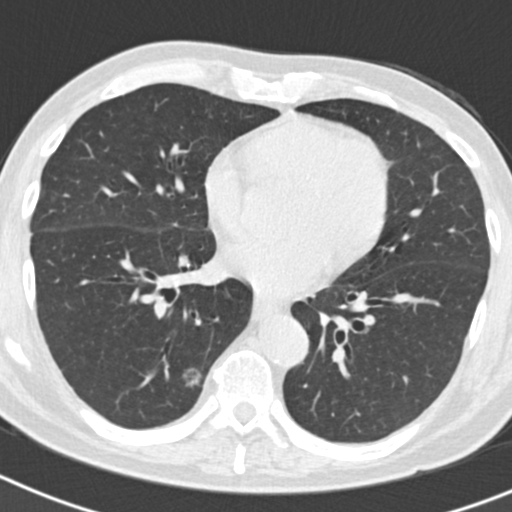
Low-dose screening chest CT, axial slice, second annual screen, lung window (W 1500 / L -600 HU), 2 mm slice thickness, standard (soft-tissue) reconstruction kernel (B30f). Male participant, aged 70 years at enrolment. Current smoker at enrolment.
Lesion marked by an expert reader, bounding box <124,356,209,429> (left, top, right, bottom; pixels). The screening reader recorded 5 non-calcified nodules or masses ≥4 mm on this exam (right lower lobe, right lower lobe, right upper lobe, right upper lobe, left upper lobe); which of them this box marks is not recorded. Official screen result: positive, other. Later outcome: lung cancer diagnosed 622 days after this screen (after the third annual screen) — bronchiolo-alveolar adenocarcinoma, NOS, right lower lobe, poorly differentiated (G3), stage IB (AJCC 6th edition), 30 mm at pathology.